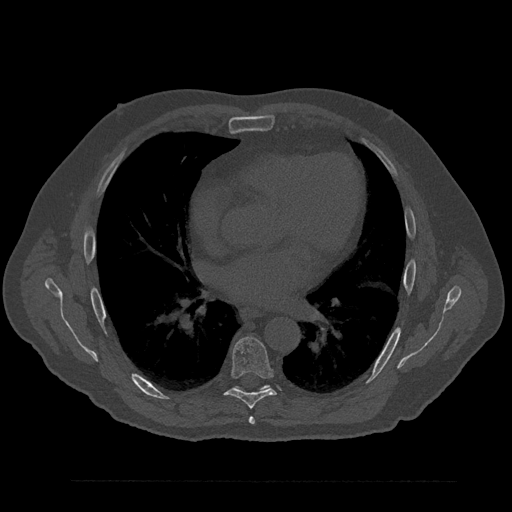
CT including the spine, one axial slice; slice 500 of 797 in the series (ordered by position); 120 kVp; bone window (W 1800 / L 400 HU); 512 × 512 image matrix, field of view 430 × 430 mm. Patient: male, 61 years. From the clinical record (not read from this slice): primary cancer: prostate.
Structures marked on this image (semi-automatic segmentation, software-assisted and operator-edited):
- T6 vertebra: box from (x=249, y=416) to (x=255, y=425) px
- T7 vertebra: (x=209, y=337)–(x=276, y=409)
- T8 vertebra: (x=234, y=385)–(x=269, y=389)